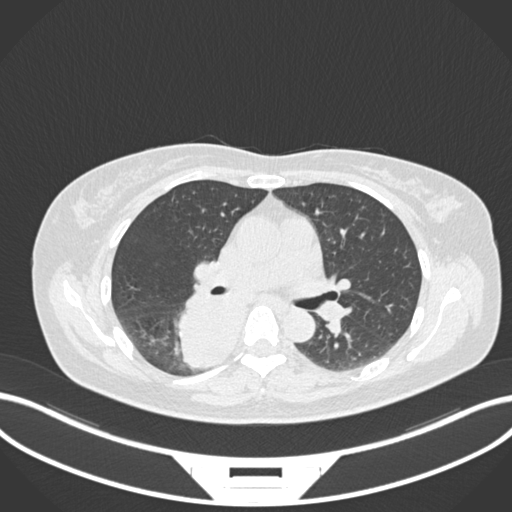
Chest CT, one axial slice. Slice 605 of 677 in the series (ordered by position). Reconstruction kernel B30f. Lung window (W 1500 / L -600 HU). 512 × 512 image matrix, field of view 400 × 400 mm. Patient: female, 54 years. Case-level facts recorded for this patient, not image findings: clinical TNM (as recorded): T4 N0 M0.
Annotated regions visible in this slice (rectangle marked by the reading radiologist):
- lung tumour (recorded histology: adenocarcinoma): bounding box (x1, y1, x2, y2) in pixels: (171, 291, 247, 373)